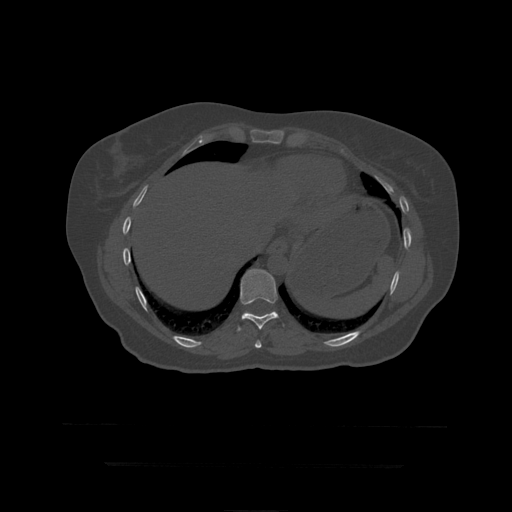
CT including the spine, one axial slice. Slice 239 of 399 in the series (ordered by position). Reconstruction kernel STANDARD. 120 kVp. Bone window (W 1800 / L 400 HU). 1.25 mm slice thickness. 512 × 512 image matrix, field of view 450 × 450 mm. Patient age 41 years. Case-level facts recorded for this patient, not image findings: primary cancer: breast.
Outlined on this slice (semi-automatic segmentation, software-assisted and operator-edited):
- T10 vertebra: bounding box (x1, y1, x2, y2) in pixels: (237, 269, 285, 331)
- T11 vertebra: (242, 313, 245, 316)
- T9 vertebra: (255, 340, 262, 350)